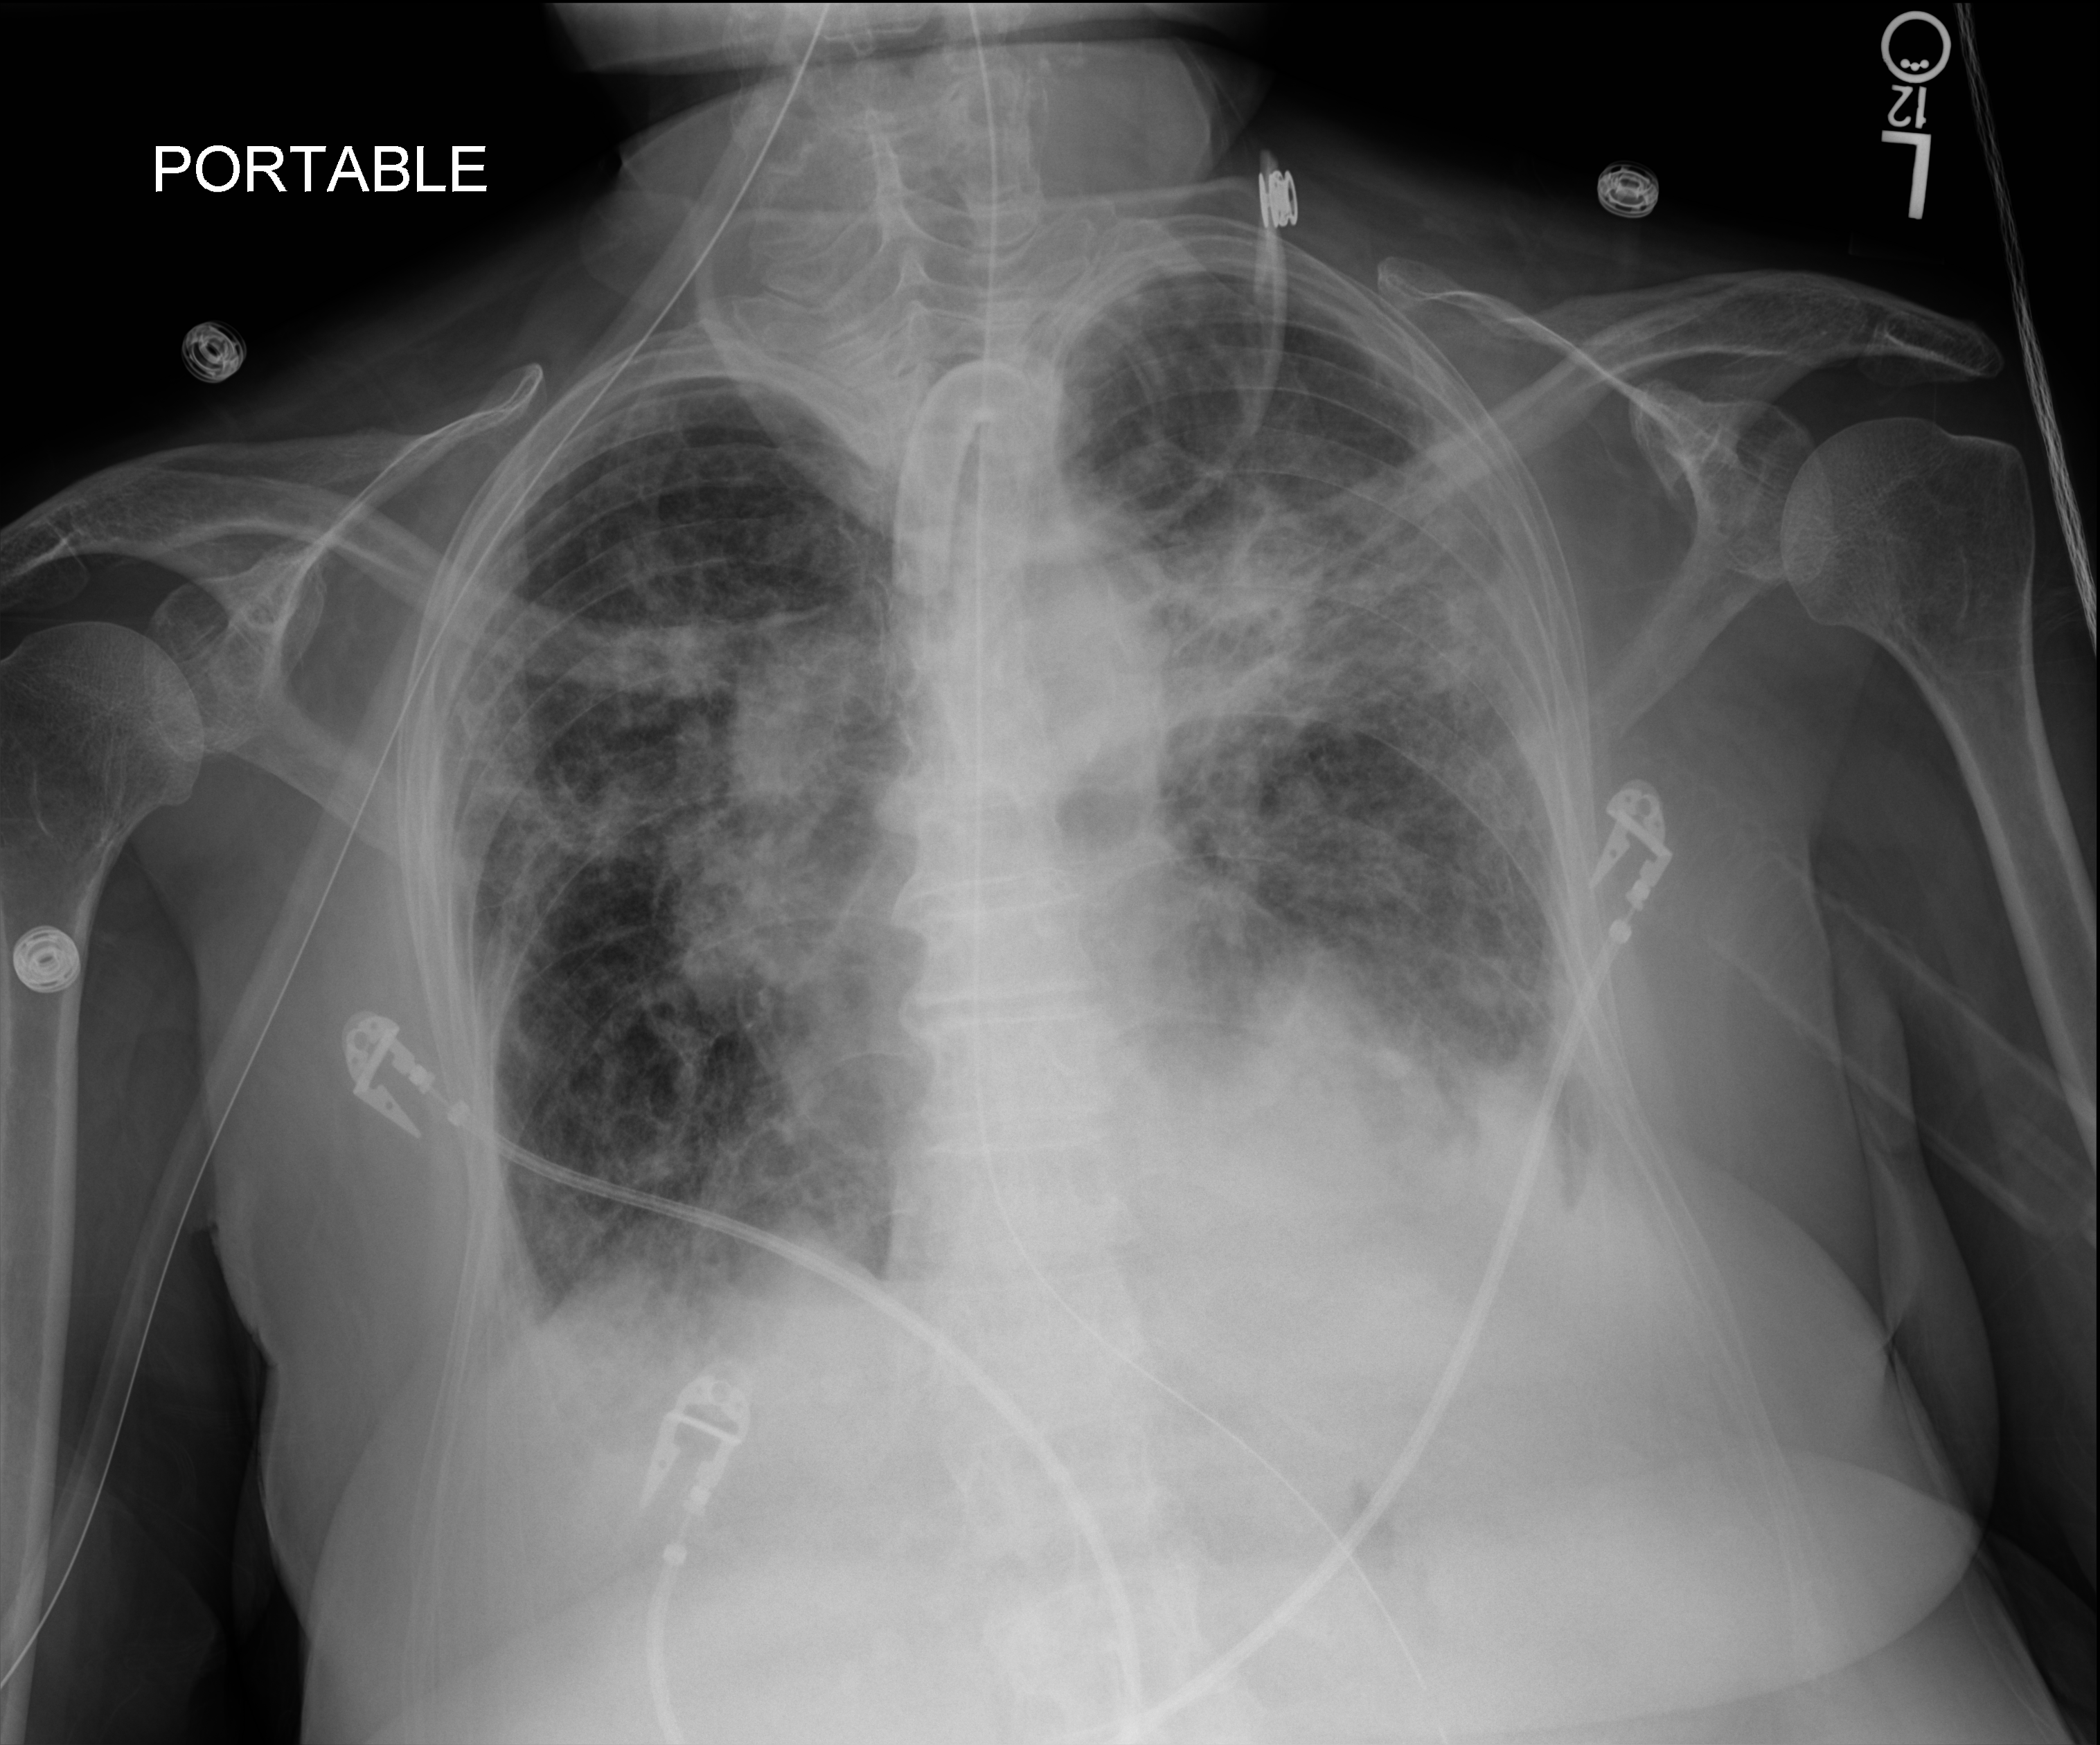
Chest X-ray (portable); anteroposterior (AP) projection. Female patient hospitalised with COVID-19, age 75–90 years.
Hospital-stay facts (about this admission, not read from this image; timing relative to this image not recorded):
- COPD (admission record): no